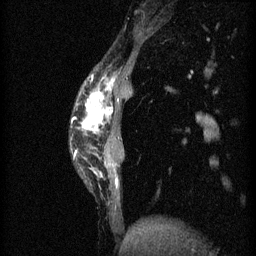
Breast MRI (dynamic contrast-enhanced), one sagittal slice. Position 11 of 60 along the scan axis. 3 images stored at this slice position (order not interpretable as contrast timing). 1.5 T. TE 4.2 ms, TR 11 ms. 256 × 256 image matrix, field of view 180 × 180 mm. Patient: female, 40 years.
Annotated regions visible in this slice (semi-automatically segmented with operator editing):
- analysis volume of interest (the breast-tissue region the enhancement analysis was run in; not a lesion): box from (x=72, y=78) to (x=133, y=191) px
- tumour enhancement mask (voxels above the 70 % enhancement threshold inside the analysis volume of interest): (x=73, y=88)–(x=119, y=187)